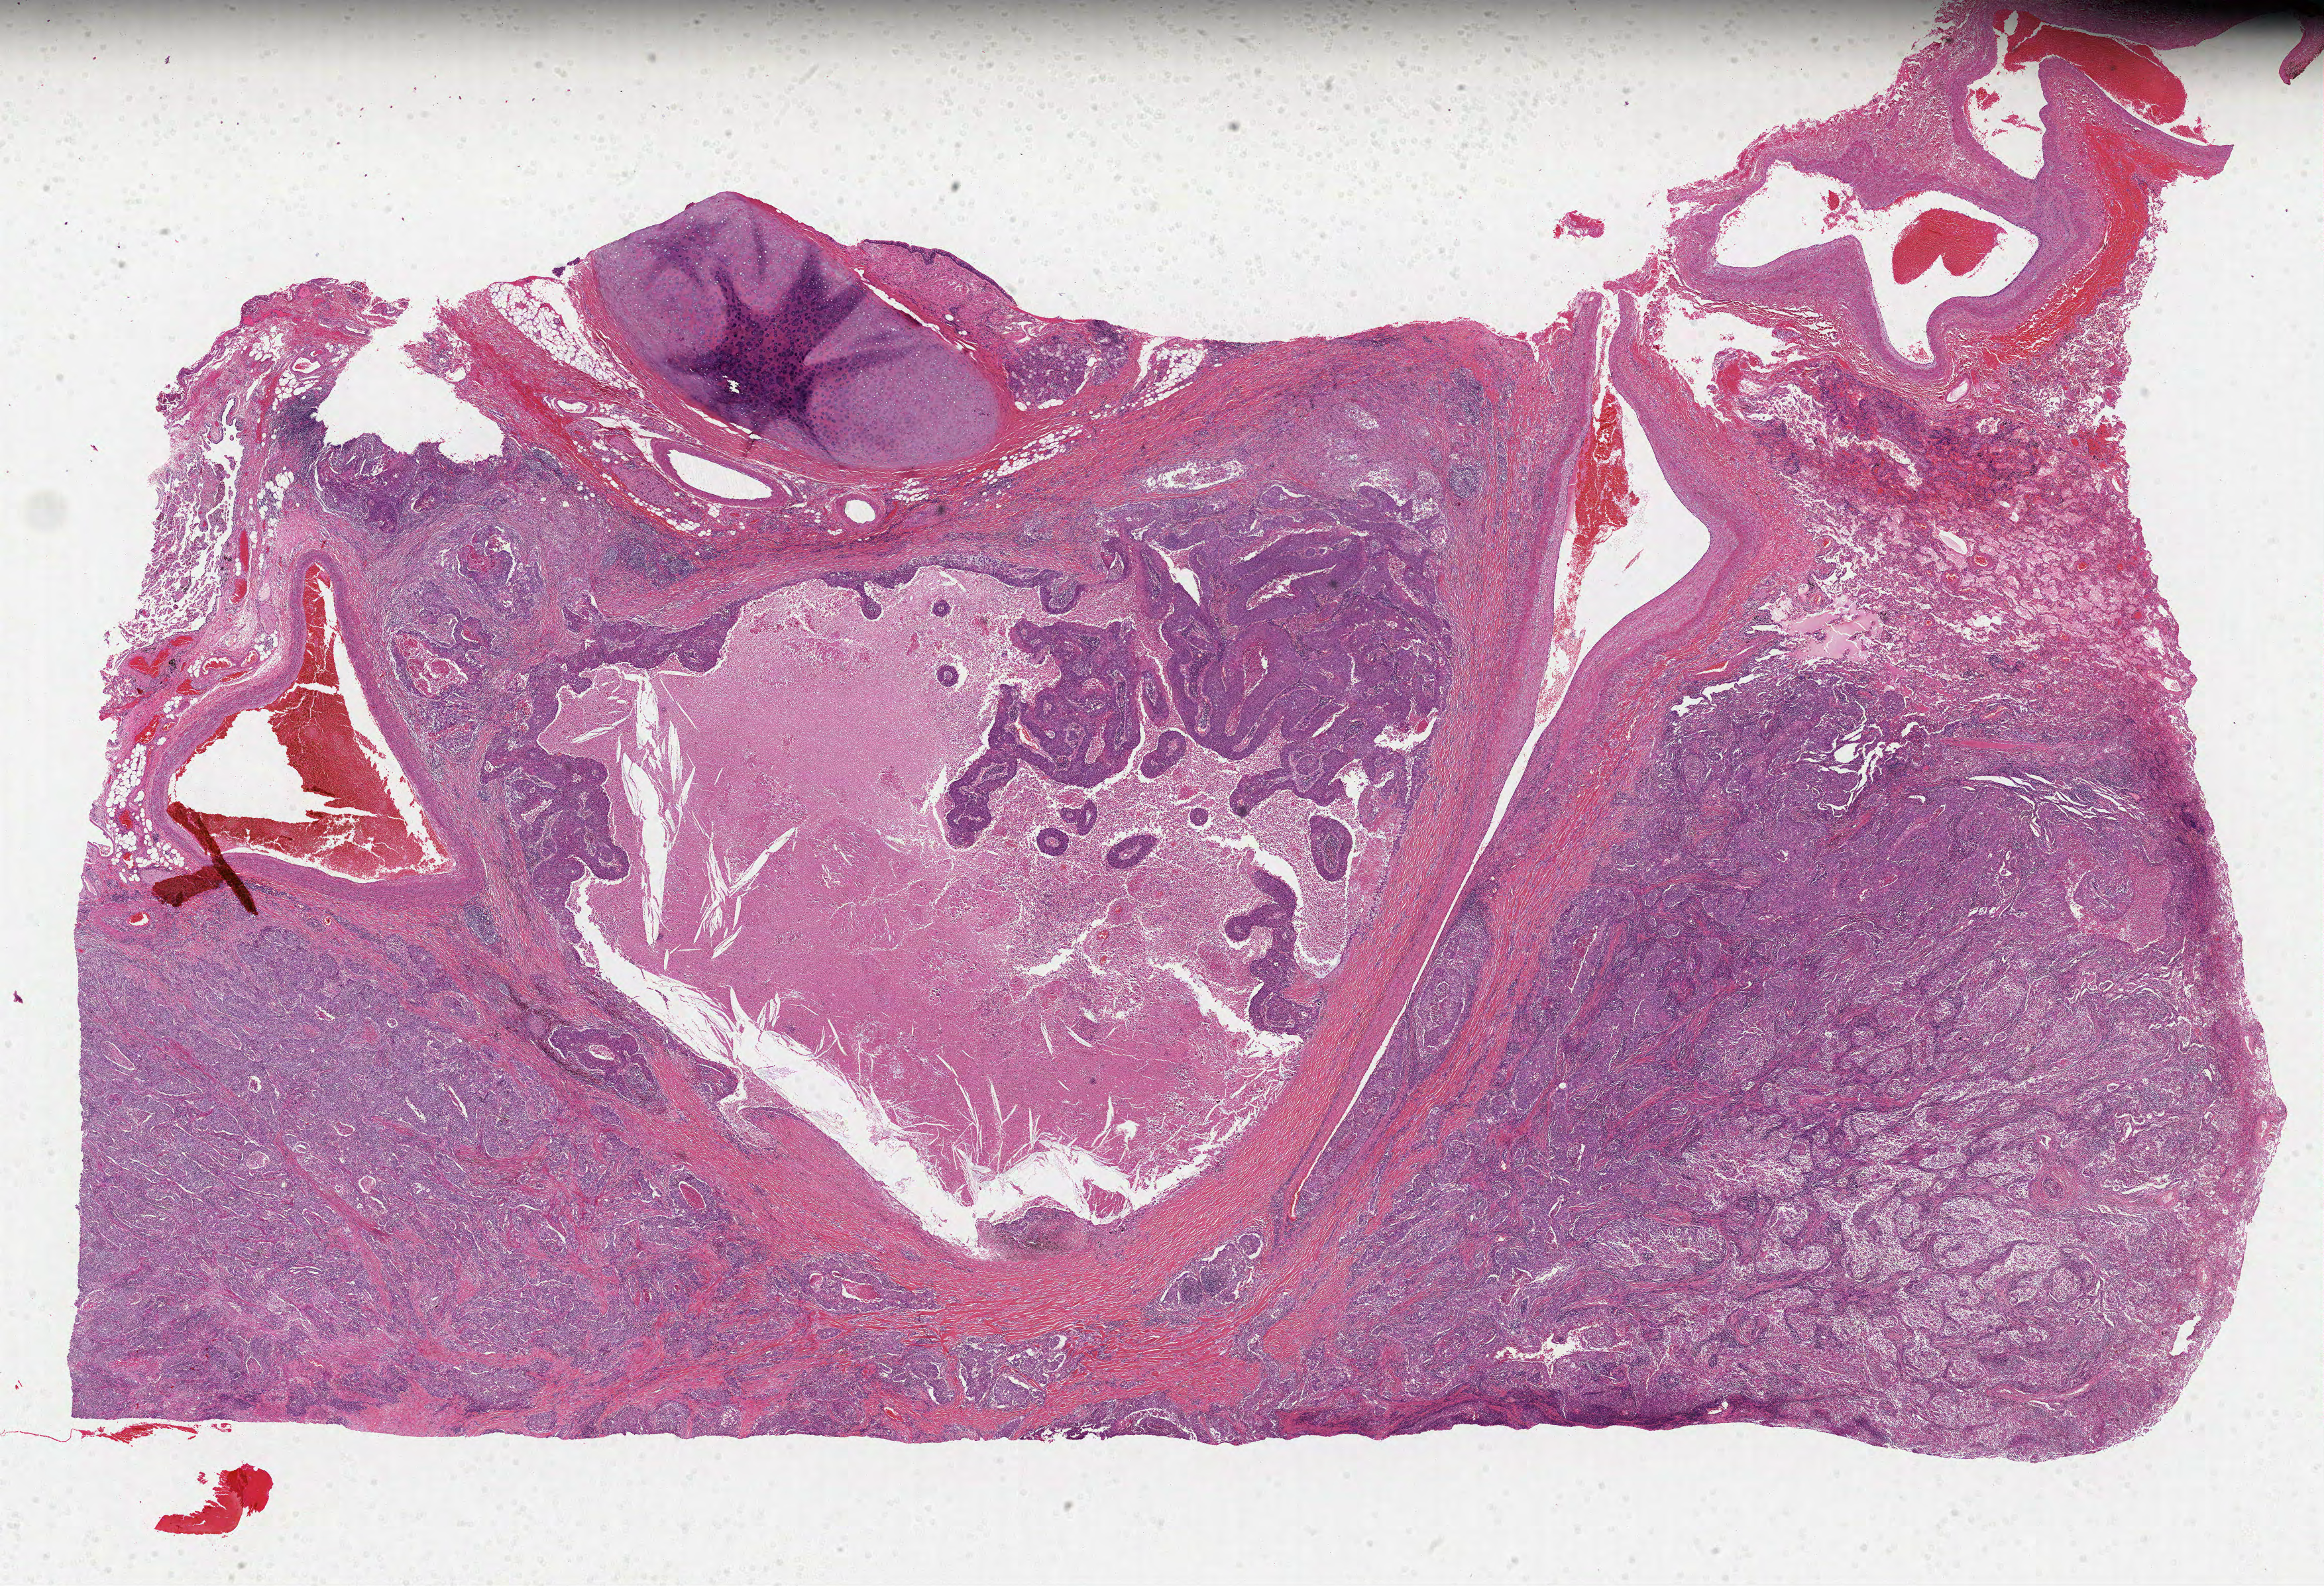
Digitized H&E-stained tissue section (whole slide) — whole scanned area (about 28.3 x 19.3 mm, slide scanned at 40x) shown as a low-resolution overview. Formalin-fixed paraffin-embedded (FFPE) diagnostic section. Lung, primary tumour sample. Male, age 58 years at initial diagnosis.
- pathologic diagnosis: Squamous cell carcinoma, NOS (upper lobe, lung)
- laterality: right
- TNM: T2a N1 M0
- AJCC pathologic stage: IIA (7th edition)